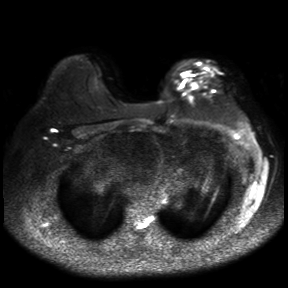
Breast MRI, one axial slice. Position 24 of 30 along the scan axis. Diffusion-weighted series; image 2 of 4 stored at this slice position (different b-values; order by instance number). 3 T. 4 mm slice thickness. 288 × 288 image matrix, field of view 360 × 360 mm. Female patient.
Annotated regions visible in this slice (manually delineated by an expert):
- tumour on diffusion-weighted imaging: bounding box (x1, y1, x2, y2) in pixels: (188, 81, 200, 92)